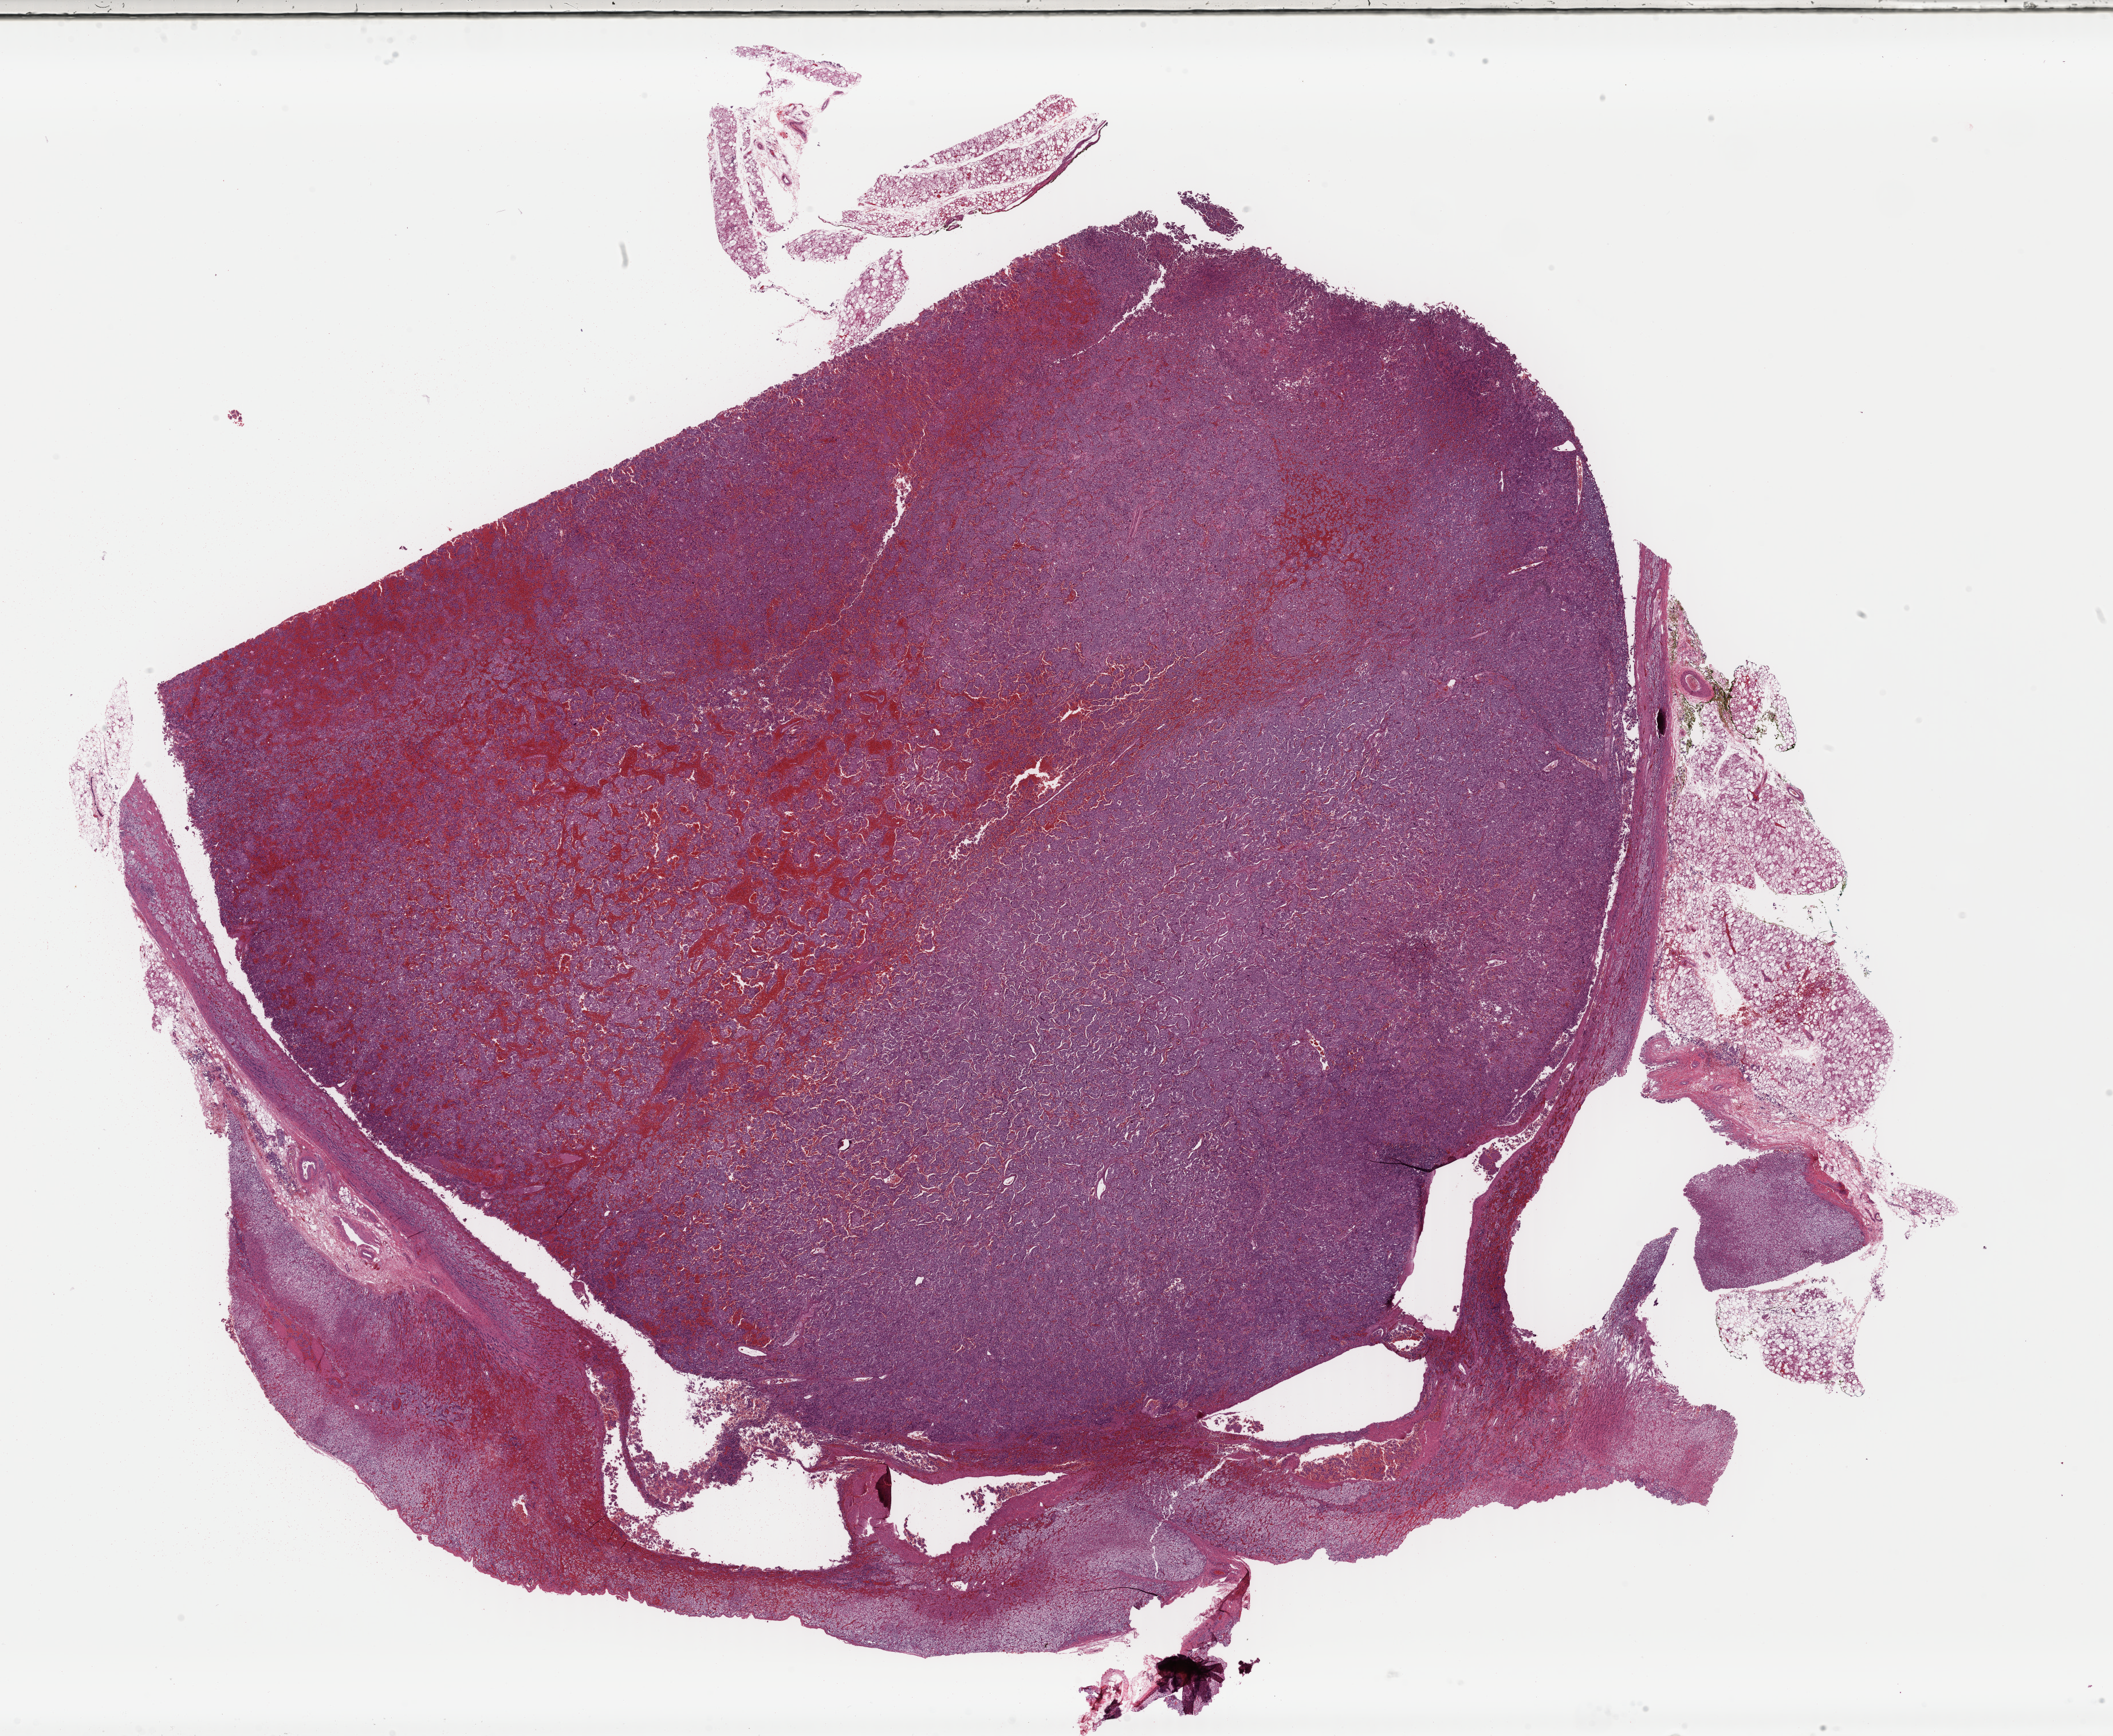
Whole-slide histology image, H&E-stained, a low-resolution overview of the entire scanned area, about 29.1 x 23.9 mm; formalin-fixed paraffin-embedded (FFPE) diagnostic section; adrenal gland, primary tumour sample. Patient: female, age at initial diagnosis 35 years.
Pathologic diagnosis: Pheochromocytoma, NOS. Laterality: right.